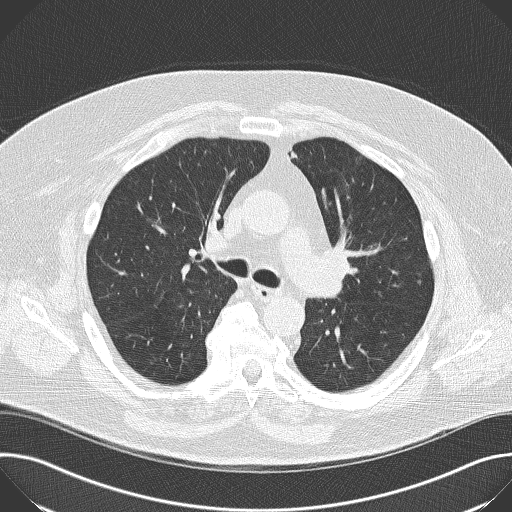
Chest CT (low-dose screening protocol), one axial image; first (baseline) screen; lung window (W 1500 / L -600 HU); 2 mm slice thickness; lung (sharp) reconstruction kernel (B50f); slice 54 of 138 in the series. Male participant, aged 68 years at enrolment. Former smoker at enrolment.
Lesion marked by an expert reader, bounding box (x1, y1, x2, y2) in pixels: (317, 230, 373, 283). The screening reader recorded 2 non-calcified nodules or masses ≥4 mm on this exam (left lower lobe, right lower lobe); which of them this box marks is not recorded. Official screen result: positive, change unspecified: nodule(s) >= 4 mm or enlarging nodule(s), mass(es), or other non-specific abnormalities suspicious for lung cancer. Participant outcome: lung cancer diagnosed 638 days after this screen (after the second annual screen) — squamous cell carcinoma, NOS, left upper lobe, poorly differentiated (G3), stage IIB (AJCC 6th edition), 35 mm at pathology.